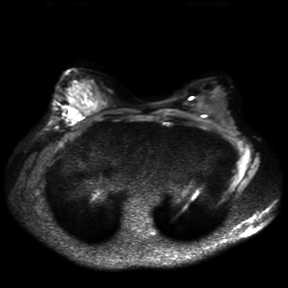
Breast MRI, one axial slice; slice 19 of 30 in the series (ordered by position); diffusion-weighted series; image 2 of 4 stored at this slice position (different b-values; order by instance number); 3 T; 4 mm slice thickness; 288 × 288 image matrix. Female patient.
Structures marked on this image (expert manual segmentation):
- tumour on diffusion-weighted imaging: bounding box <66,109,81,121> (left, top, right, bottom; pixels)